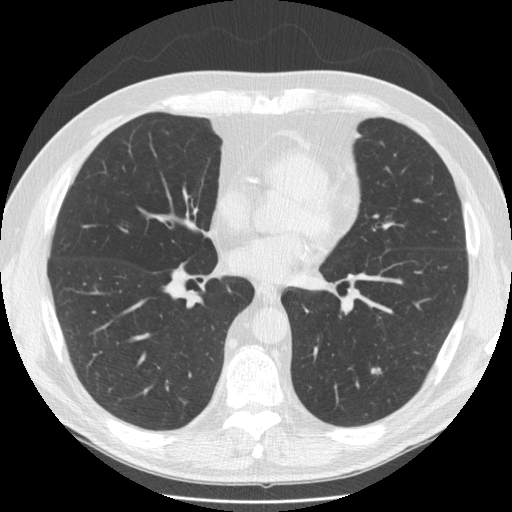
Chest CT (low-dose screening protocol), one axial image, third annual screen, lung window (W 1500 / L -600 HU), 2.5 mm slice thickness, 512 × 512 image matrix, field of view 360 × 360 mm. Male, age 58 years at enrolment.
Expert reader's lesion annotation, box from (x=361, y=358) to (x=399, y=385) px. Reader record for this screening exam (exam-level; its link to the box is not recorded): non-calcified nodule or mass ≥4 mm, left lower lobe, 10 × 7 mm, smooth margins, soft tissue attenuation, pre-existing on the prior screen: yes; interval growth: yes. Participant outcome: lung cancer diagnosed 49 days after this screen — adenocarcinoma, NOS, left lower lobe, poorly differentiated (G3), stage IA (AJCC 6th edition), 8 mm at pathology.